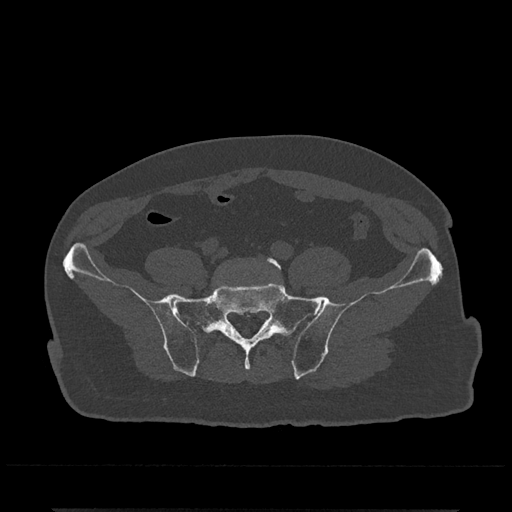
CT including the spine, one axial slice; slice 34 of 797 in the series (ordered by position); bone window (W 1800 / L 400 HU); 512 × 512 image matrix, field of view 393 × 393 mm. Patient: male, 67 years. From the clinical record (not read from this slice): primary cancer: prostate.
Structures marked on this image (semi-automatically segmented with operator editing):
- L5 vertebra: bounding box <227,257,281,270> (left, top, right, bottom; pixels)